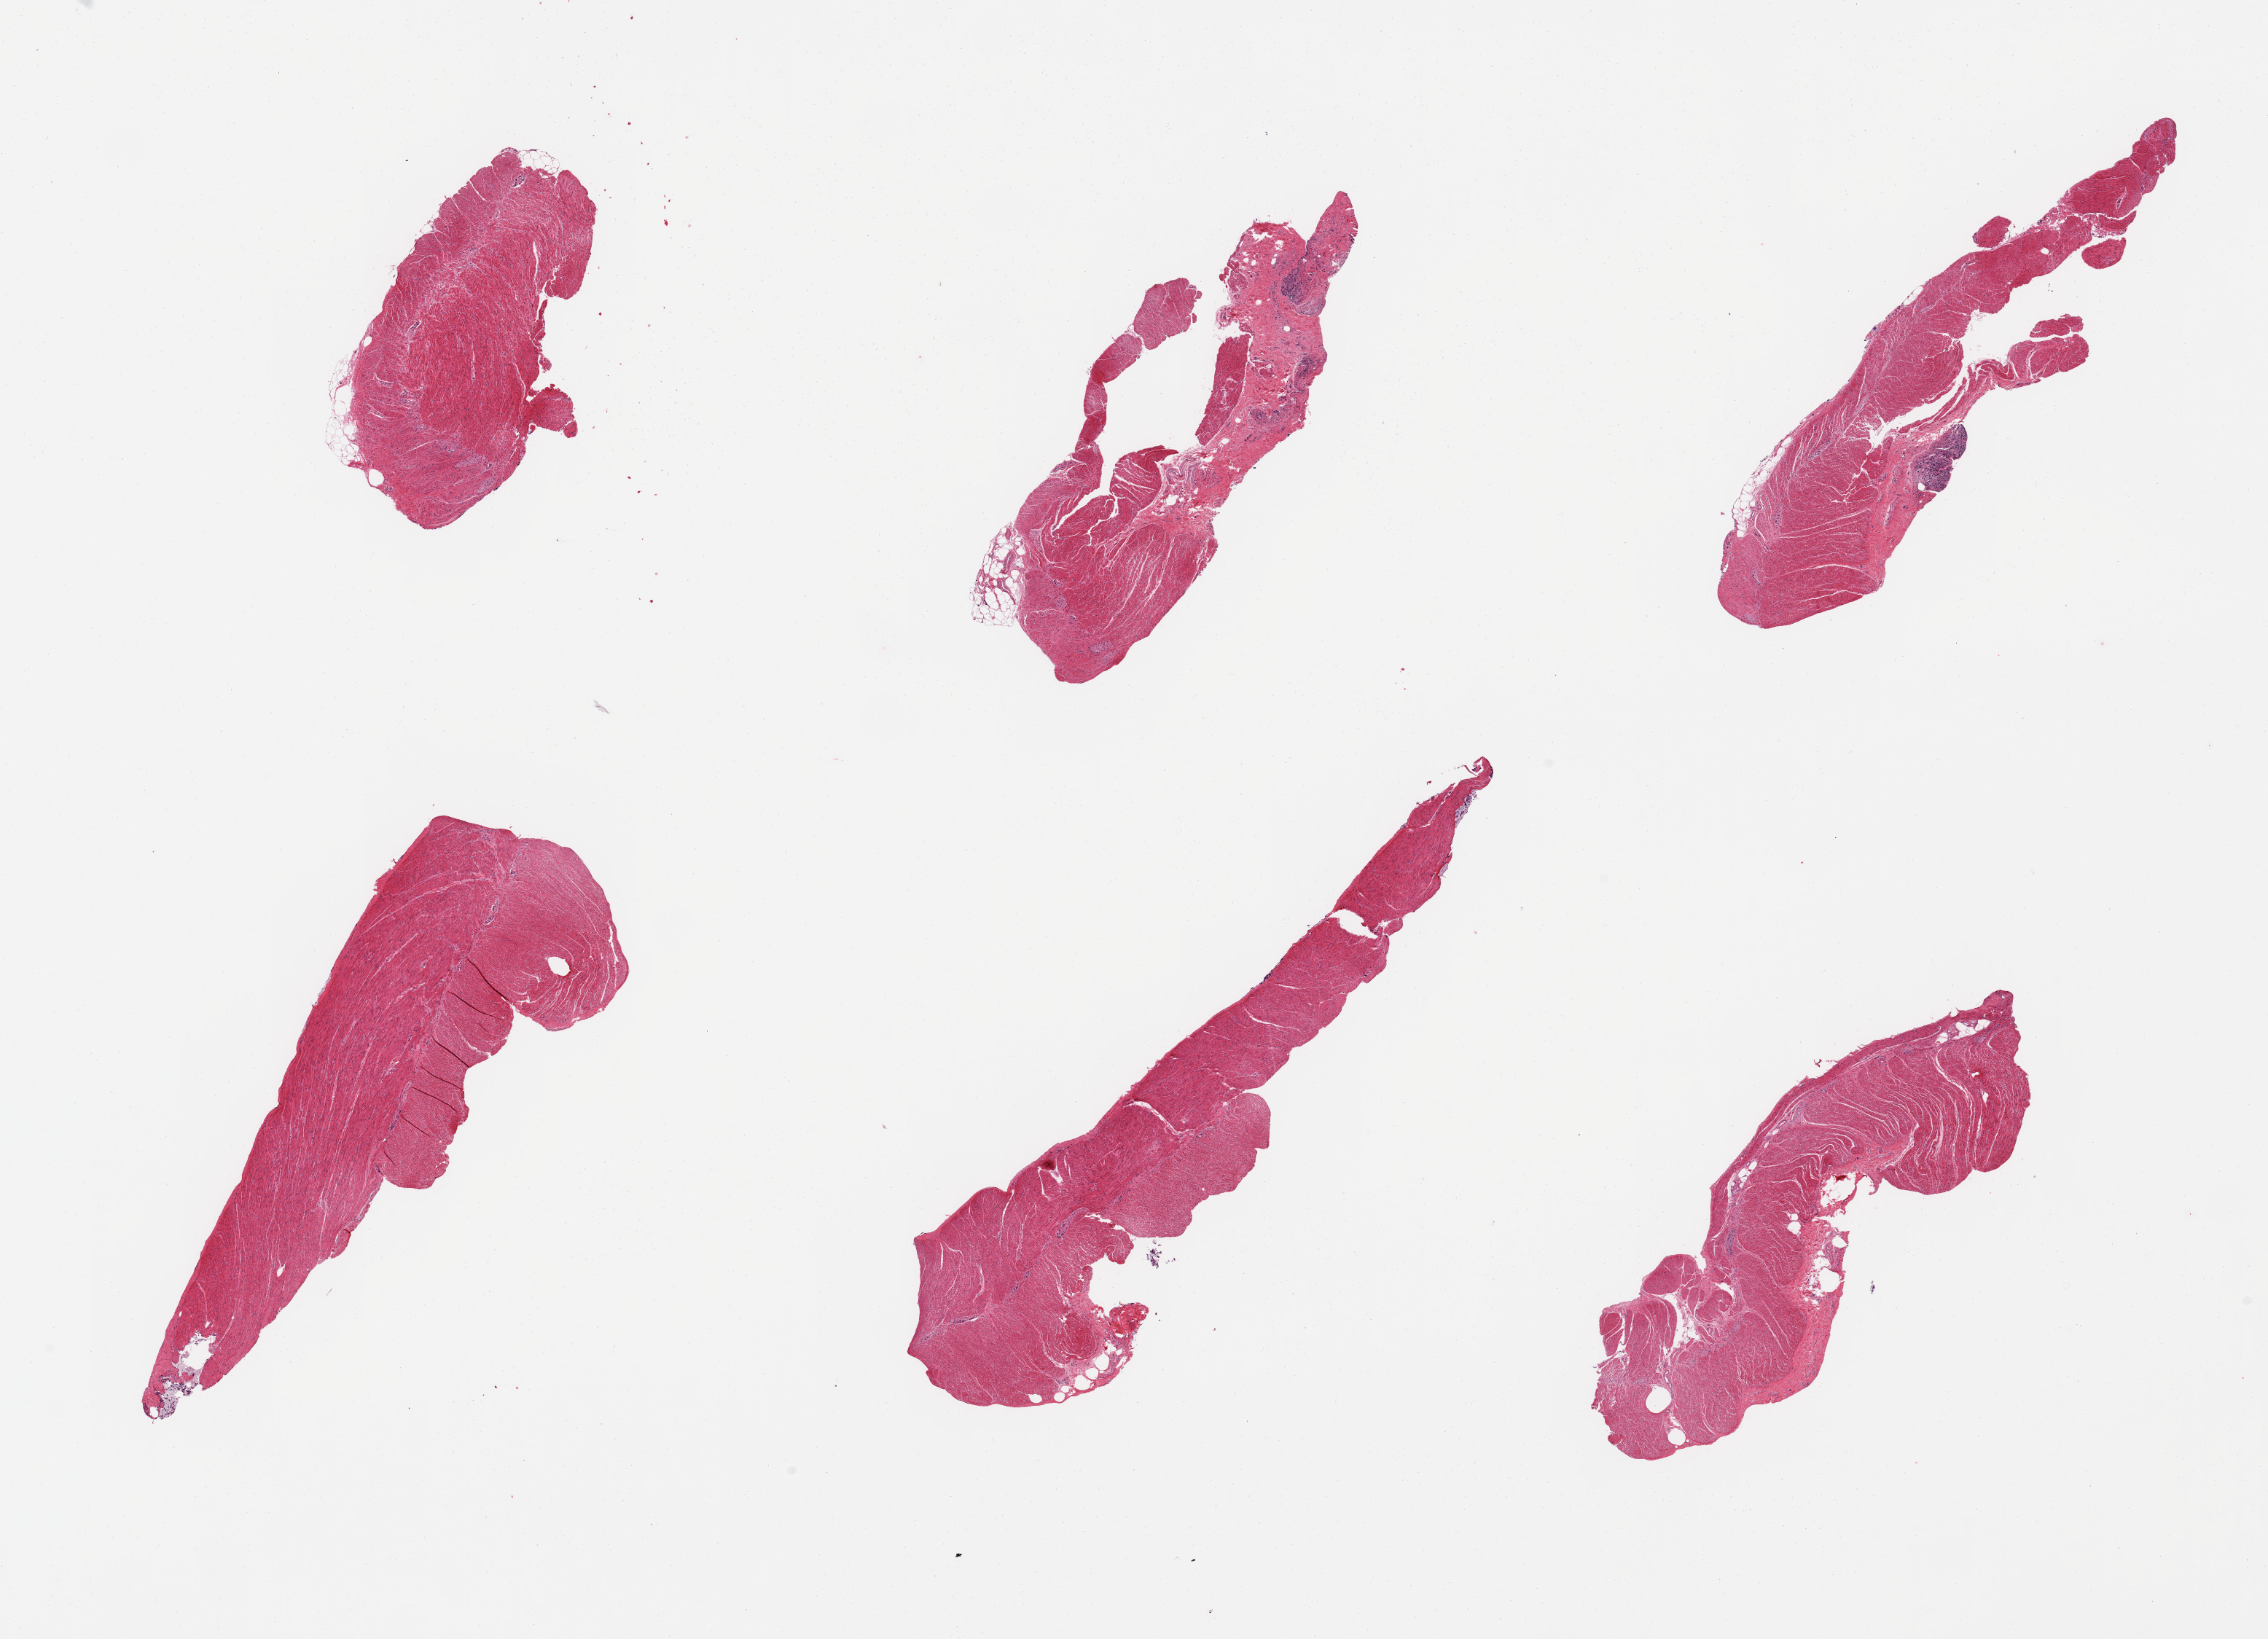
Whole-slide image, hematoxylin and eosin (H&E) stain, brightfield — a low-resolution overview of the entire scanned area, about 24.6 x 17.8 mm, PAXgene-fixed paraffin-embedded (PFPE) section, sampled site (target tissue): sigmoid colon, tissue donor sample. Donor sex: male.
- reviewer comment on this tissue sample: 6 pieces, confirmed target muscularis, minute nubbin of autolyzed mucosa